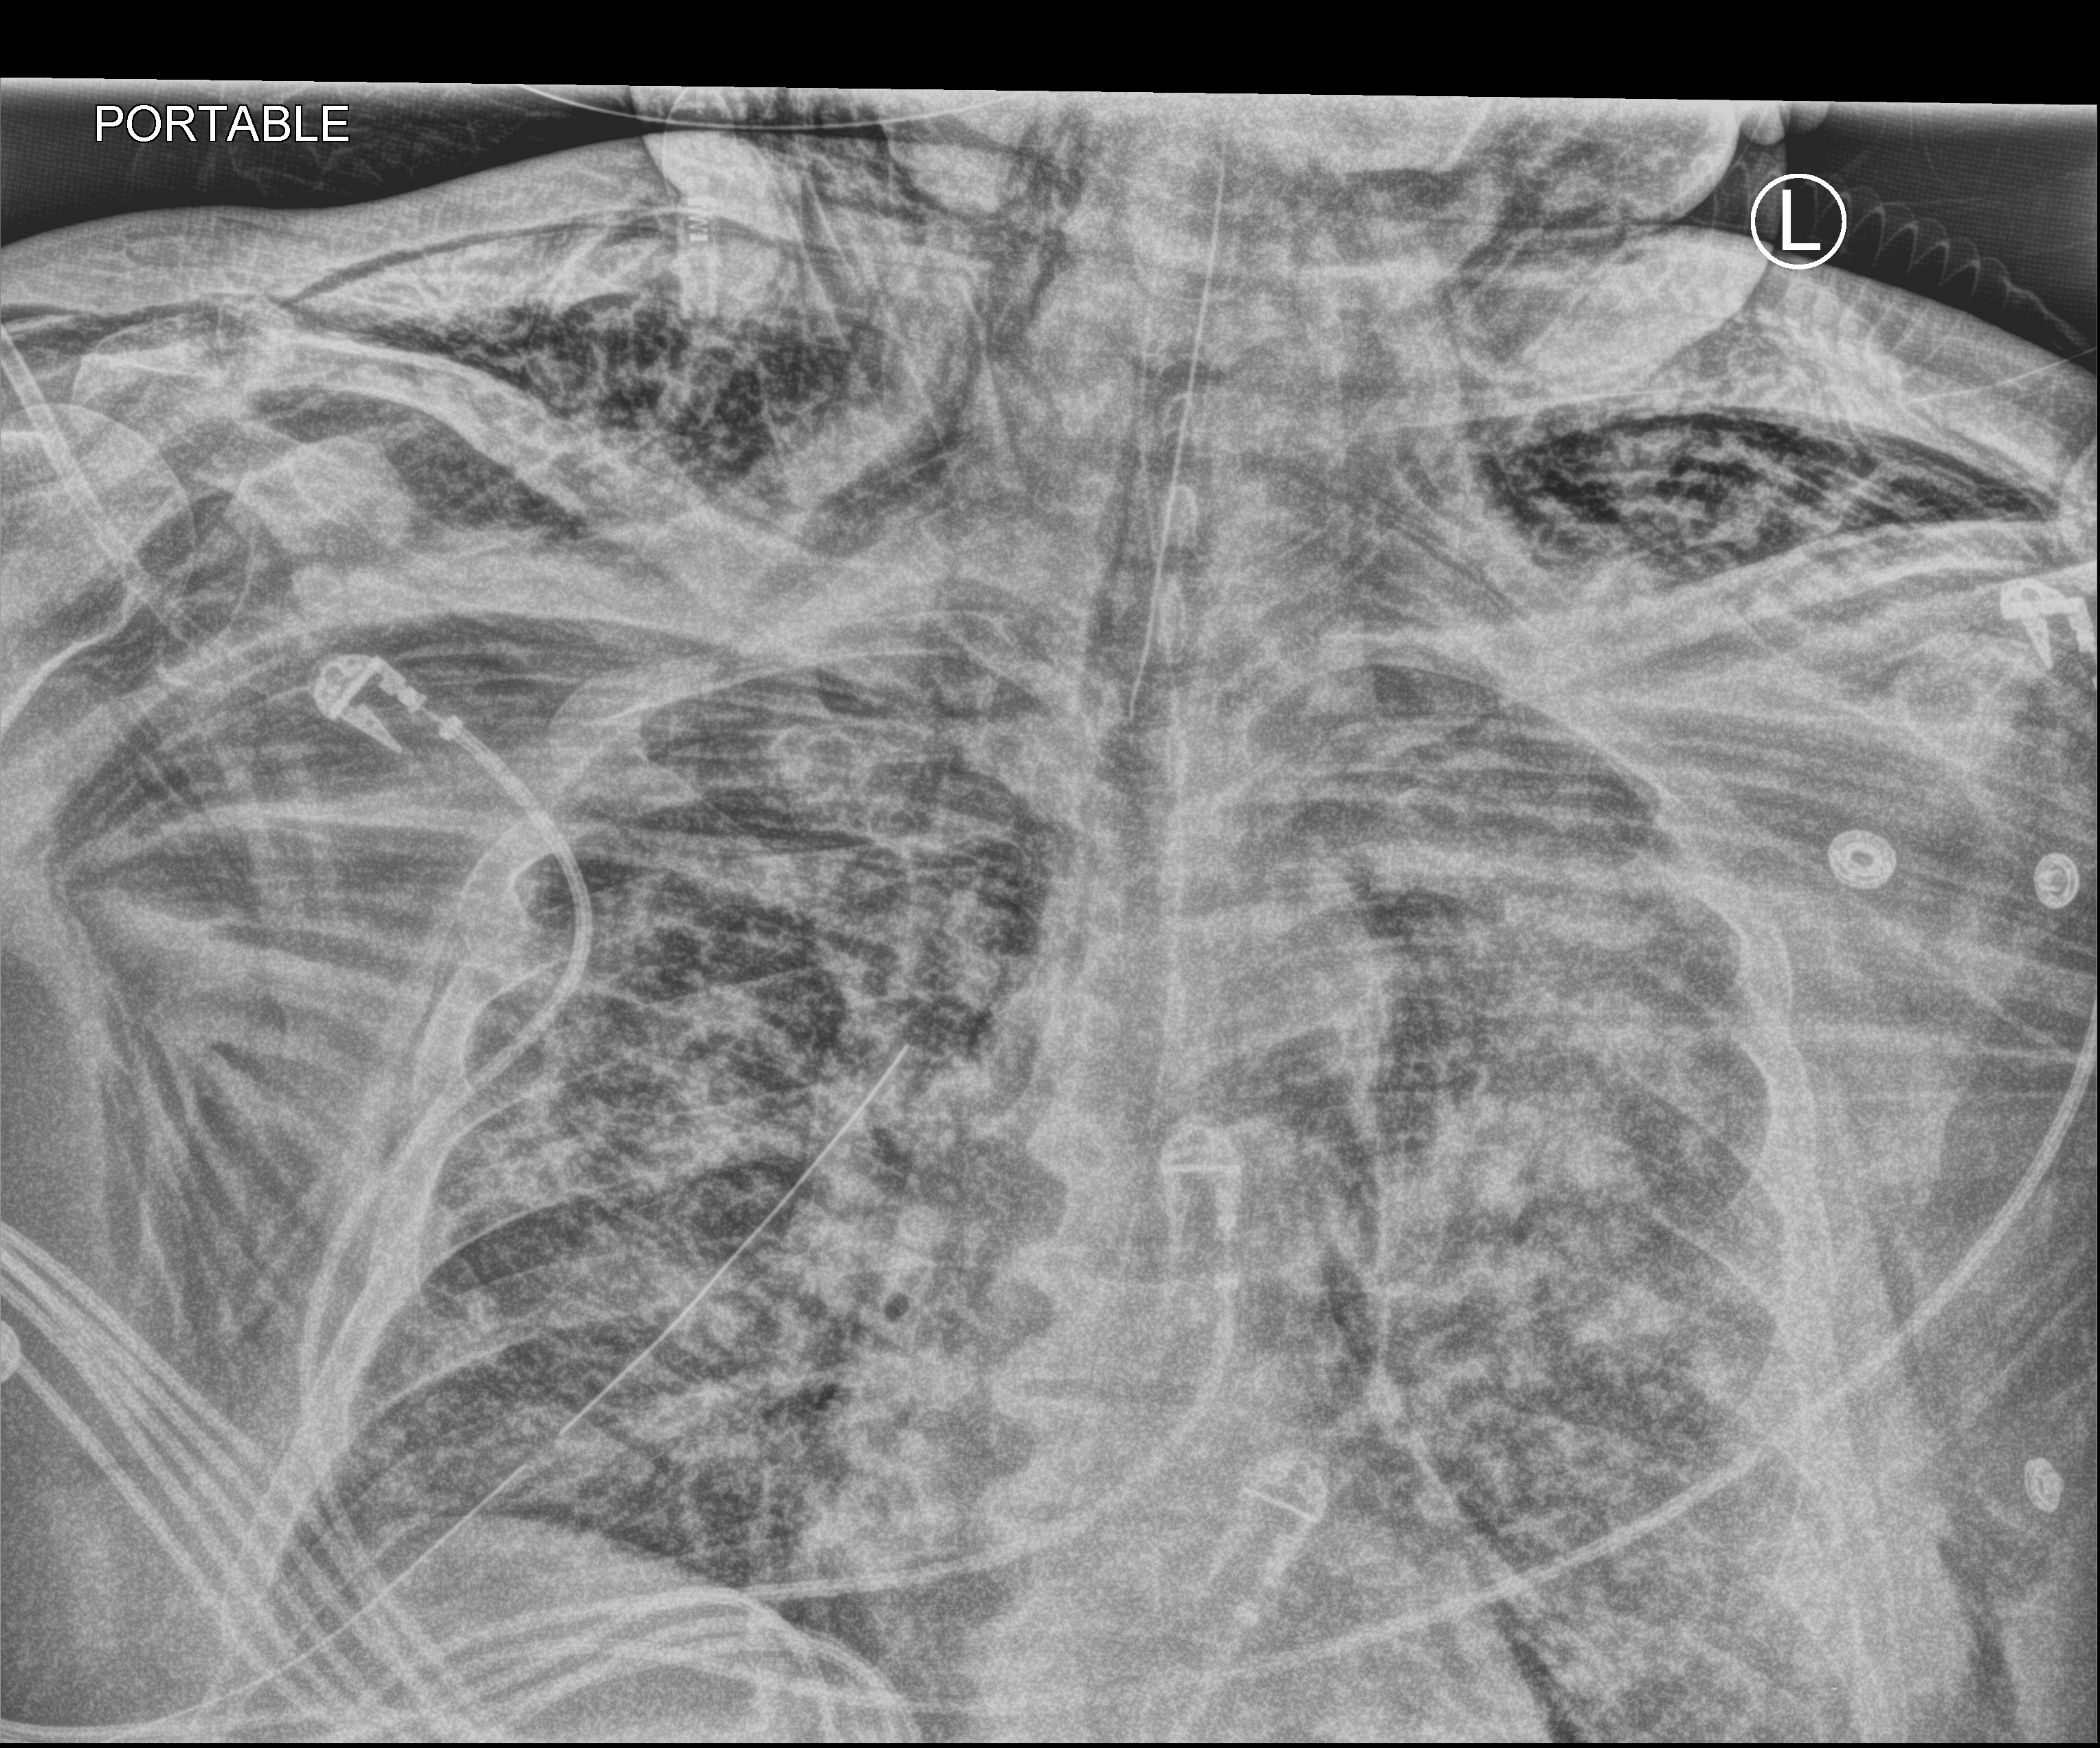
Chest X-ray (portable), anteroposterior (AP) projection. Adult patient hospitalised with COVID-19, age 18–59 years.
From the hospital-stay record, not from the radiograph (when in the stay this image was taken is not recorded): admitted to intensive care during this hospital stay: yes.